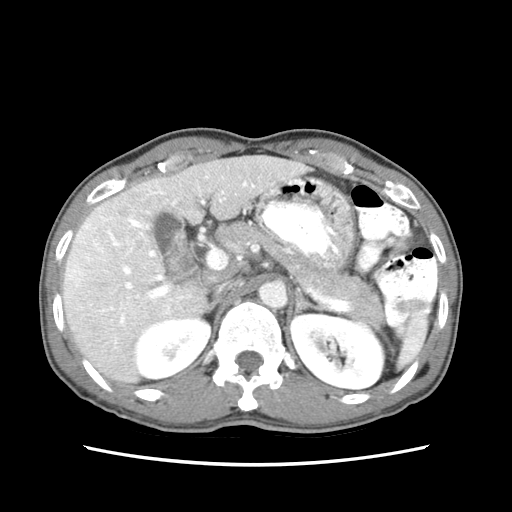
Contrast-enhanced abdominal CT (liver protocol), one axial slice. 120 kVp. Soft-tissue window (W 400 / L 40 HU). 2.5 mm slice thickness. 512 × 512 image matrix. From the clinical record (not read from this slice): diagnosis: hepatocellular carcinoma (patient treated with transarterial chemoembolisation; whether this scan precedes or follows treatment is not stated here); TNM stage (as recorded): Stage-IIIB; Child-Pugh class: A.
Structures marked on this image (semi-automatic segmentation, software-assisted and operator-edited):
- liver parenchyma outside the tumour (the mass and vessels are separate outlines, so this box may not span the whole liver): bounding box (x1, y1, x2, y2) in pixels: (62, 154, 308, 392)
- mass: (66, 248, 107, 280)
- liver vessels: (65, 166, 298, 348)